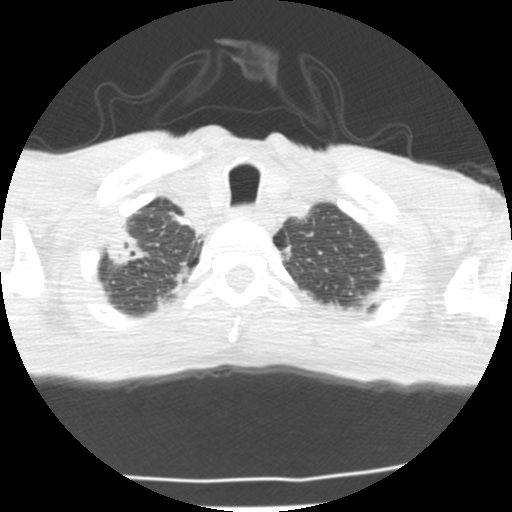
Low-dose screening chest CT, one axial slice; slice 192 of 214 in the series (ordered by position); reconstruction kernel STANDARD; 120 kVp; lung window (W 1500 / L -600 HU); 2.5 mm slice thickness; 512 × 512 image matrix, field of view 283 × 283 mm.
Outlined on this slice (manually delineated by an expert):
- lesion 1 (tumor, upper lobe of right lung): bounding box (x1, y1, x2, y2) in pixels: (108, 230, 147, 267)